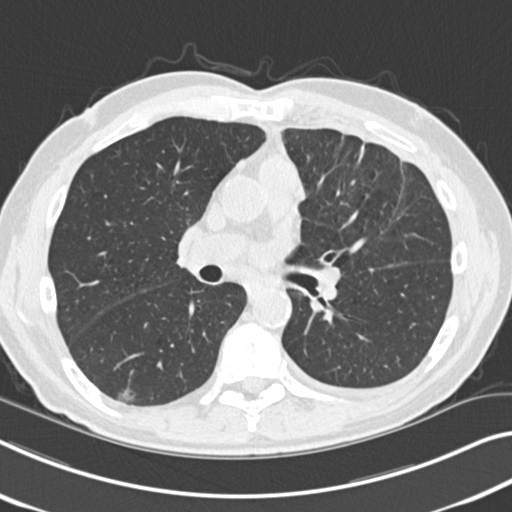
Chest CT (low-dose screening protocol), one axial image, first (baseline) screen, lung window (W 1500 / L -600 HU), 2 mm slice thickness, slice 104 of 212 in the series, 512 × 512 image matrix. Male, age 68 years at enrolment. Current smoker at enrolment.
Expert-annotated lung lesion, bounding box (x1, y1, x2, y2) in pixels: (95, 378, 146, 416). Screening reader's record for this exam (one nodule recorded; not confirmed to be the boxed lesion): non-calcified nodule or mass ≥4 mm, right lower lobe, 14 × 10 mm, poorly defined margins, ground glass attenuation. Later outcome: lung cancer diagnosed 1018 days after this screen — non-small cell carcinoma, right lower lobe, poorly differentiated (G3), stage IA (AJCC 6th edition), 23 mm at pathology.